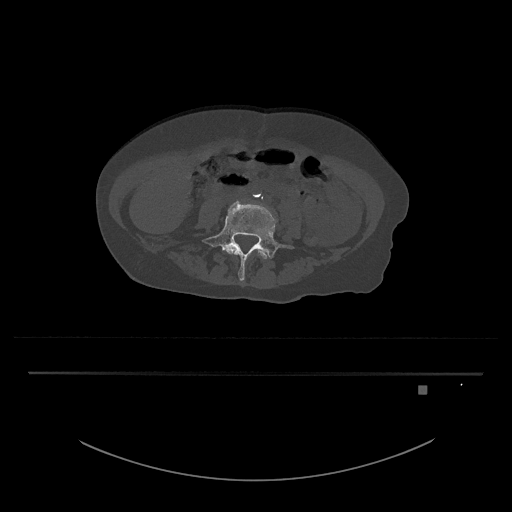
CT including the spine, one axial slice. 120 kVp. Bone window (W 1800 / L 400 HU). 512 × 512 image matrix, field of view 500 × 500 mm. Patient: female, 57 years. From the clinical record (not read from this slice): primary cancer: cervical.
Structures marked on this image (semi-automatic segmentation, software-assisted and operator-edited):
- L4 vertebra: bounding box <224,245,269,259> (left, top, right, bottom; pixels)